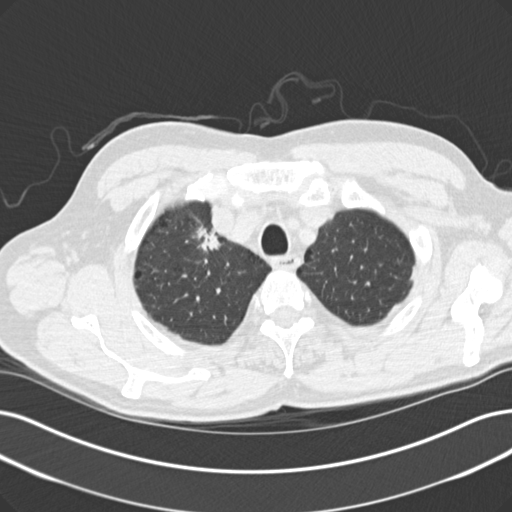
Low-dose screening chest CT, one axial slice; position 126 of 152 along the scan axis; reconstruction kernel B30f; lung window (W 1500 / L -600 HU); 2 mm slice thickness; 512 × 512 image matrix.
Annotated regions visible in this slice (expert manual segmentation):
- lesion 1 (tumor, upper lobe of right lung): bounding box <197,226,221,251> (left, top, right, bottom; pixels)